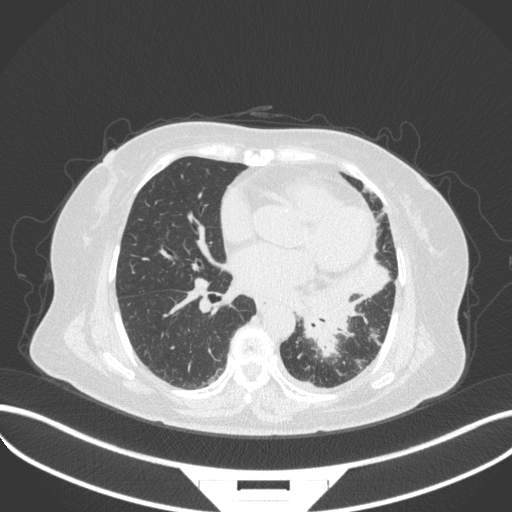
Chest CT, one axial slice. Slice 158 of 328 in the series (ordered by position). Reconstruction kernel B31f. 120 kVp. Lung window (W 1500 / L -600 HU). 1 mm slice thickness. 512 × 512 image matrix, field of view 400 × 400 mm. Female patient, age 69 years. Case-level facts recorded for this patient, not image findings: clinical TNM (as recorded): T2b N3 M1.
Structures marked on this image (rectangle marked by the reading radiologist):
- lung tumour (recorded histology: adenocarcinoma): bounding box <290,269,359,360> (left, top, right, bottom; pixels)